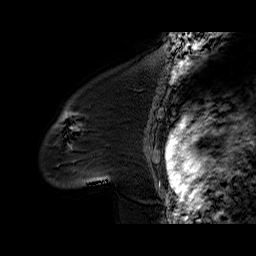
Breast MRI (dynamic contrast-enhanced), one sagittal slice. Slice 48 of 60 in the series (ordered by position). Dynamic contrast-enhanced series, time point 2 of 6 at this slice position (early post-contrast). 1.5 T. TE 6.2 ms, TR 32.4 ms. 4 mm slice thickness. 256 × 256 image matrix, field of view 200 × 200 mm. Female patient. From the clinical record (not read from this slice): setting: breast cancer imaged before/during neoadjuvant chemotherapy; receptor status: triple-negative.
Outlined on this slice (semi-automatic segmentation, software-assisted and operator-edited):
- analysis volume of interest (the breast-tissue region the enhancement analysis was run in; not a lesion): bounding box (x1, y1, x2, y2) in pixels: (41, 97, 134, 188)
- tumour enhancement mask (voxels above the 100 % enhancement threshold inside the analysis volume of interest): (67, 113, 78, 150)